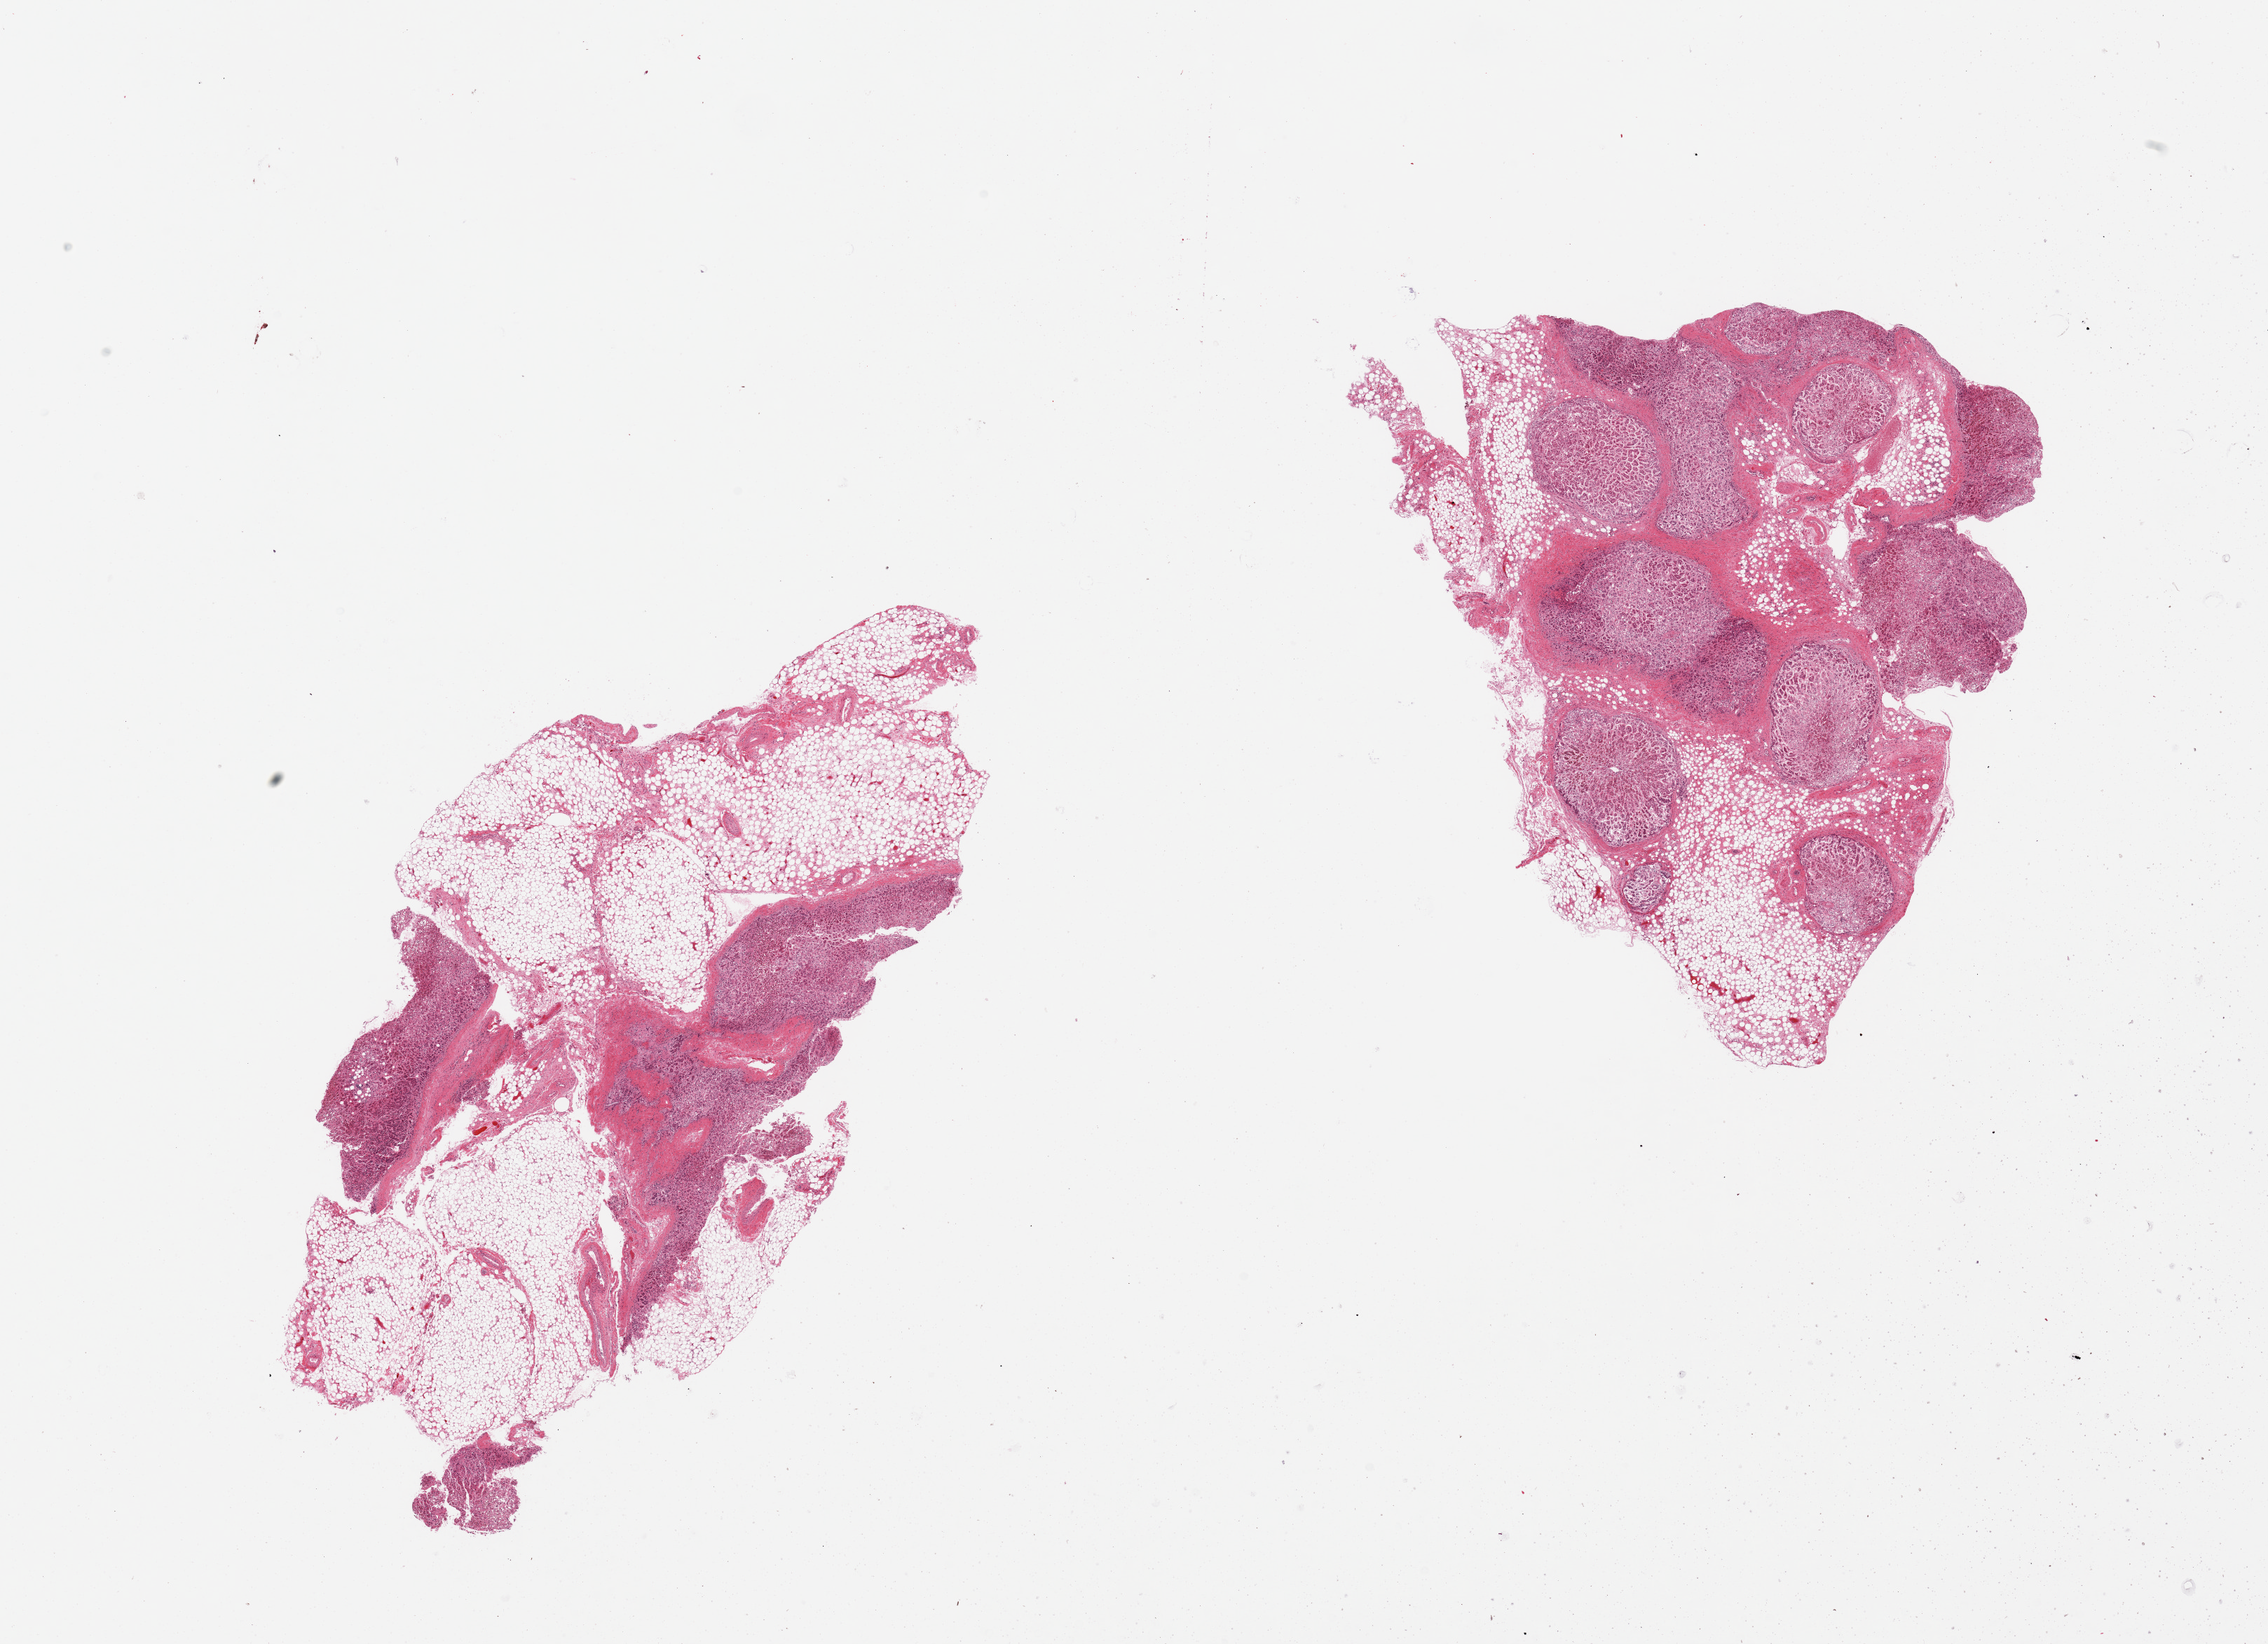
Digitized H&E-stained section, brightfield, whole scanned area (about 25.6 x 18.6 mm) shown as a low-resolution overview. PAXgene-fixed, paraffin-embedded tissue. Sampled site (target tissue): adrenal gland. Donor tissue sample. Donor: male.
Pathologist's review note for this sample: 2 pieces; one with 75% external fat.